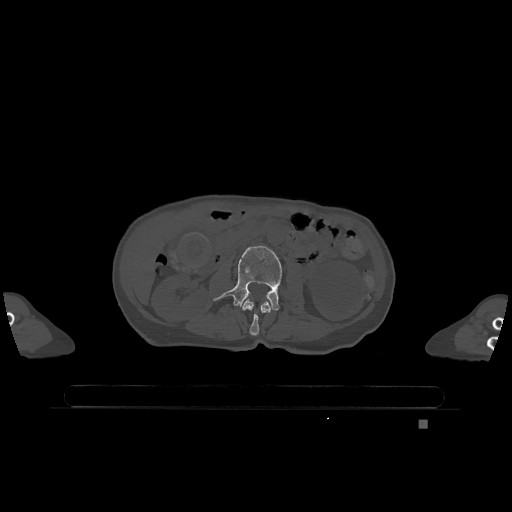
CT including the spine, one axial slice; position 376 of 1317 along the scan axis; bone window (W 1800 / L 400 HU); 0.5 mm slice thickness; 512 × 512 image matrix. Patient: female, 74 years. From the clinical record (not read from this slice): primary cancer: lung.
Annotated regions visible in this slice (semi-automatically segmented with operator editing):
- L2 vertebra: bounding box [x1, y1, x2, y2] px = [241, 299, 276, 336]
- L3 vertebra: [213, 246, 282, 310]